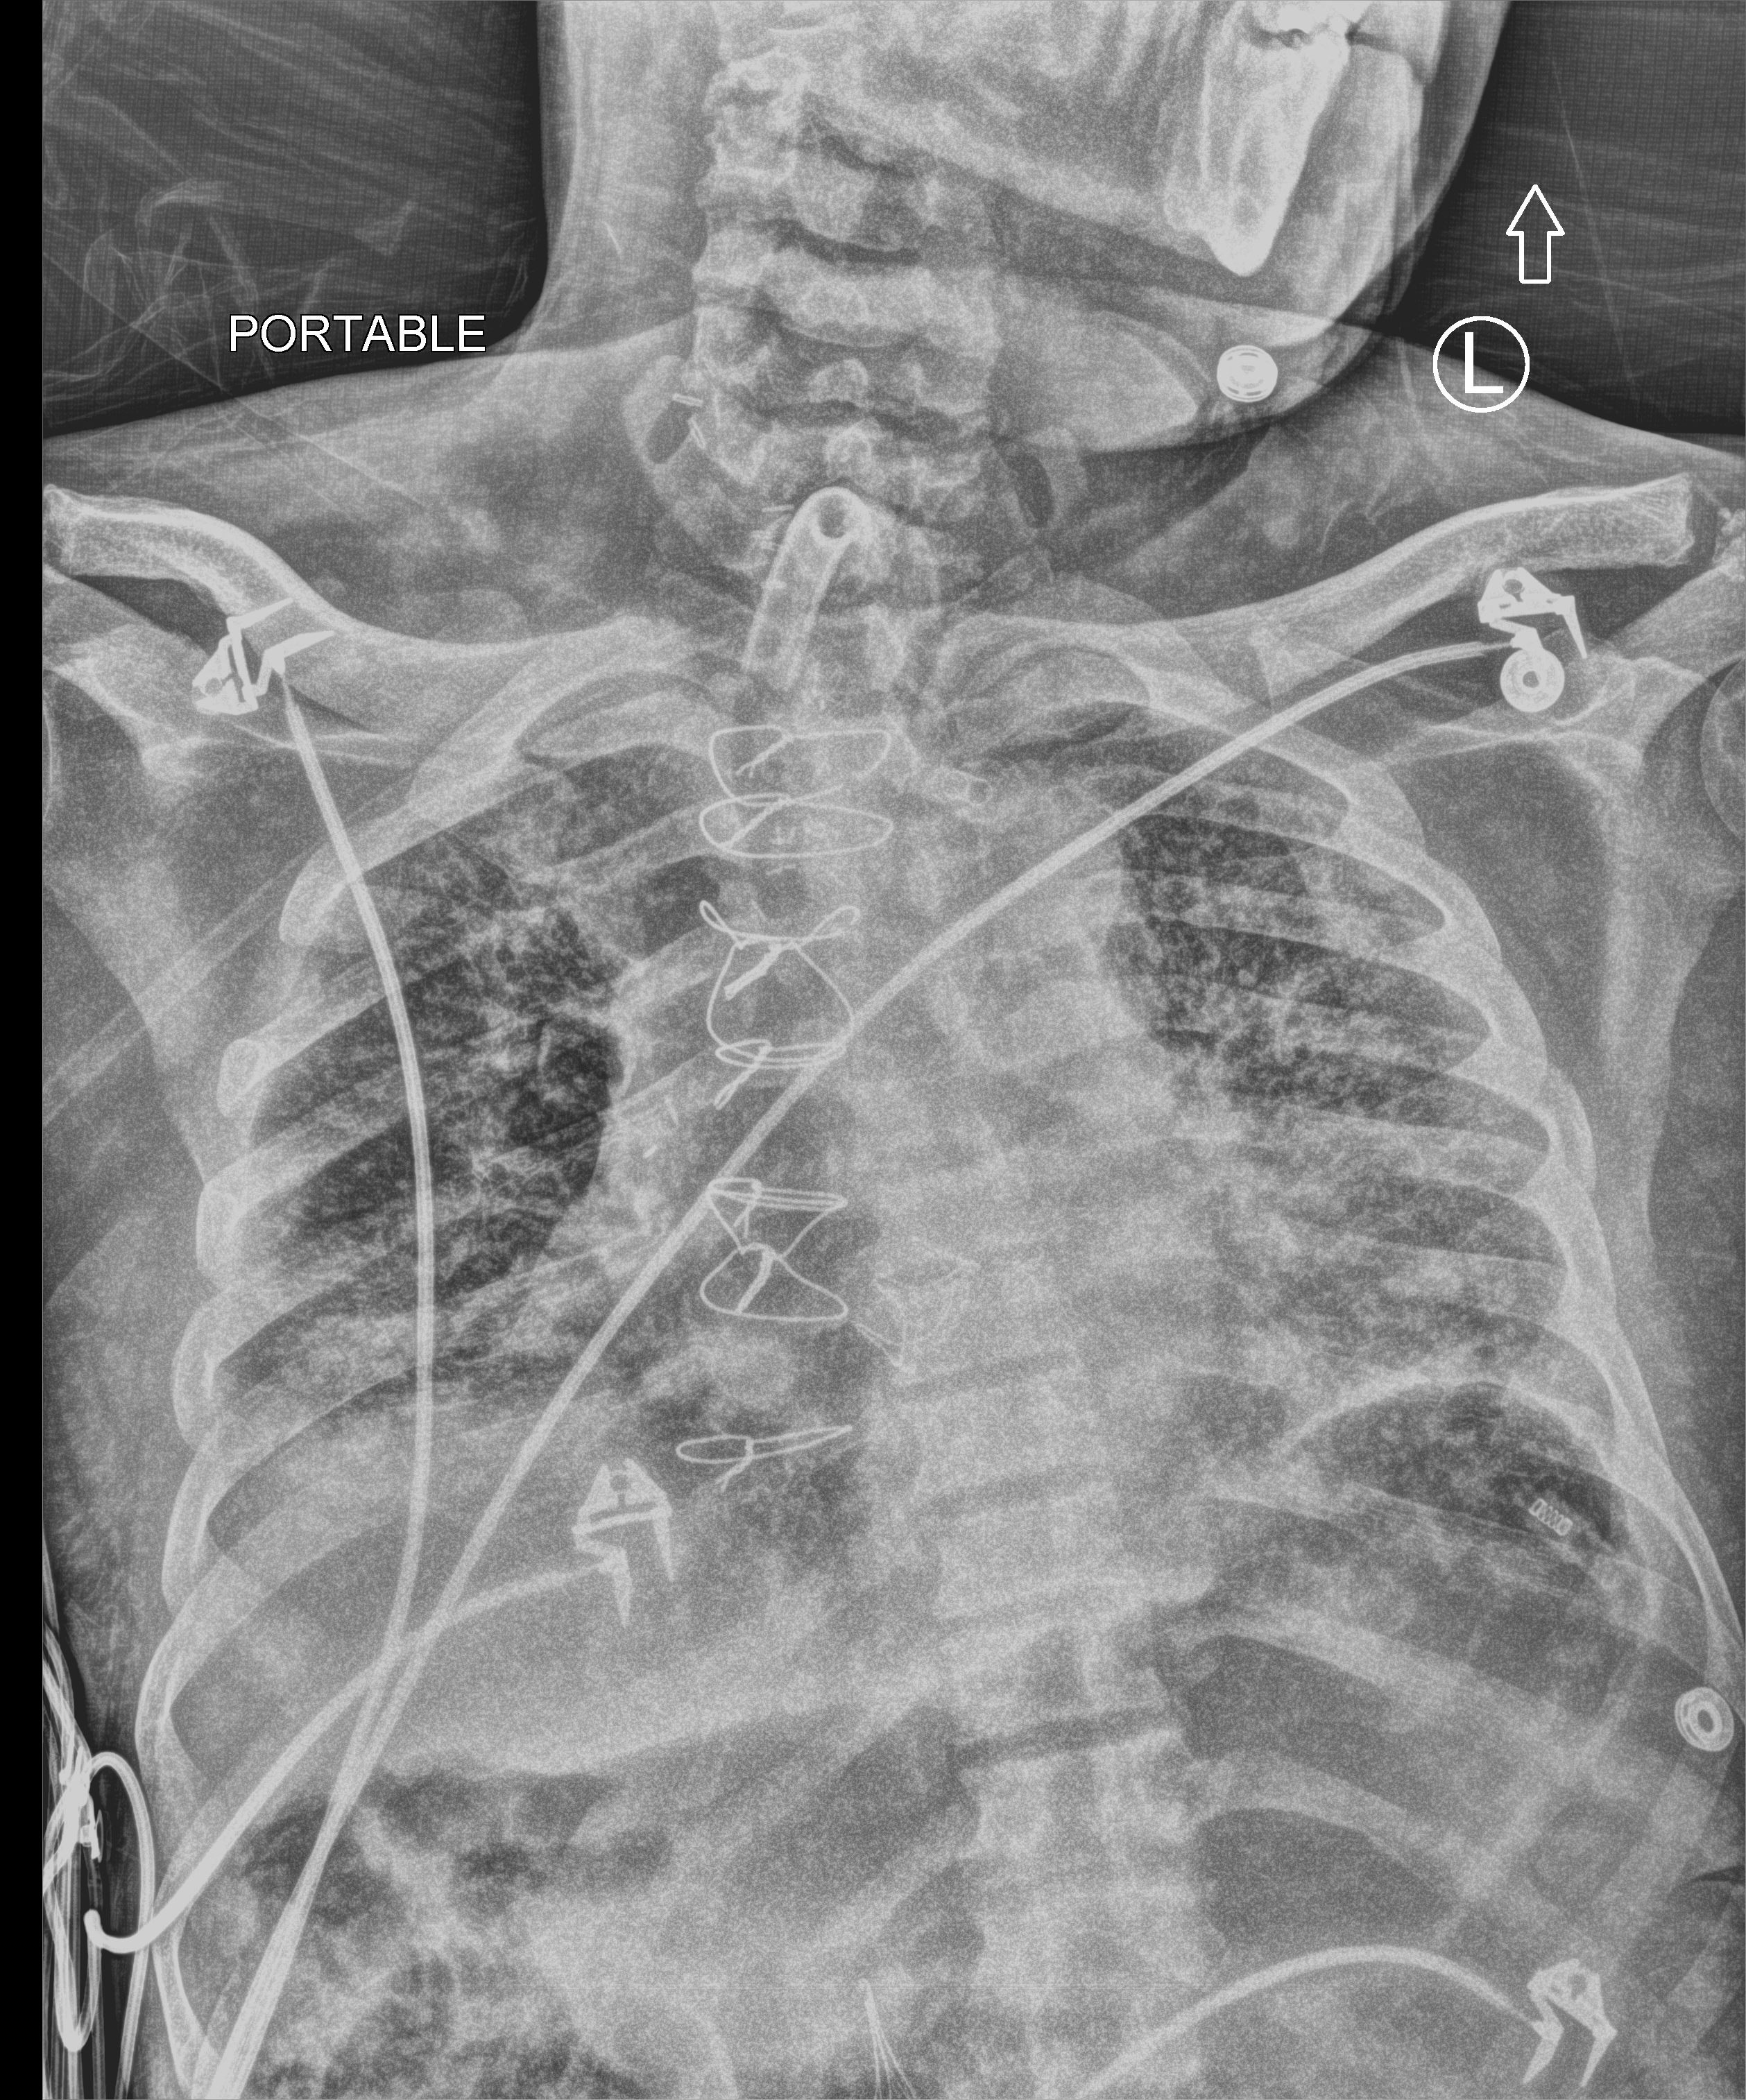
Portable chest radiograph; anteroposterior (AP) projection. Male patient hospitalised with COVID-19, age 60–74 years.
Hospital-stay facts (about this admission, not read from this image; timing relative to this image not recorded):
- mechanically ventilated during this hospital stay: yes